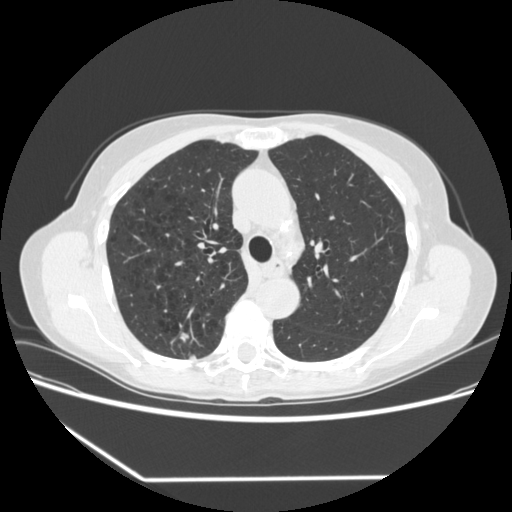
Low-dose screening chest CT, one axial slice. Position 233 of 323 along the scan axis. Reconstruction kernel STANDARD. 120 kVp. Lung window (W 1500 / L -600 HU). 1.25 mm slice thickness. 512 × 512 image matrix, field of view 360 × 360 mm.
Outlined on this slice (manually delineated by an expert):
- lesion 1 (tumor, upper lobe of right lung): bounding box <180,332,189,342> (left, top, right, bottom; pixels)